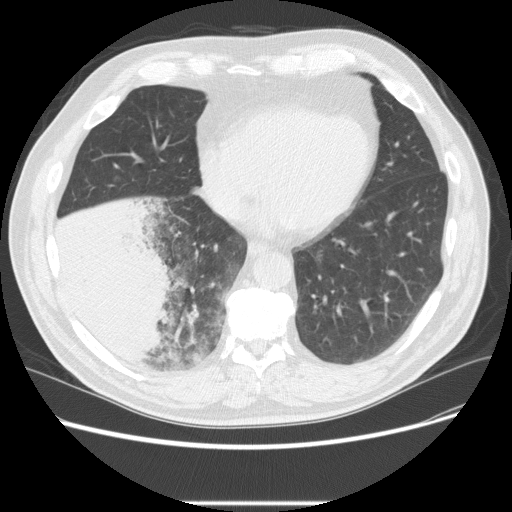
Low-dose screening chest CT, one axial slice; 120 kVp; lung window (W 1500 / L -600 HU); 2.5 mm slice thickness; 512 × 512 image matrix, field of view 380 × 380 mm.
Structures marked on this image (expert manual segmentation):
- lesion 3 (tumor, lower lobe of right lung): bounding box <54,197,180,366> (left, top, right, bottom; pixels)